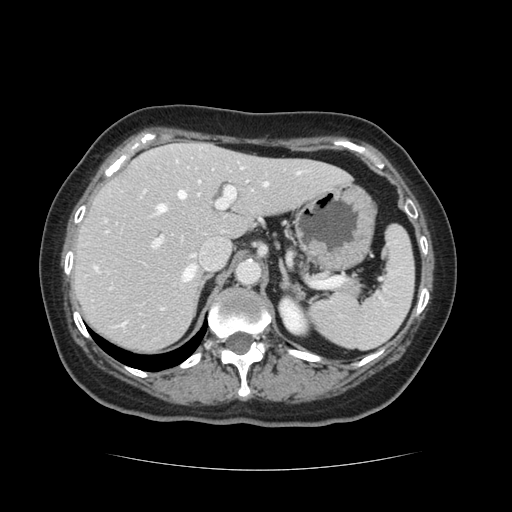
Contrast-enhanced abdominal CT, one axial slice; position 85 of 128 along the scan axis; 120 kVp; intravenous contrast given; soft-tissue window (W 400 / L 40 HU); 2.5 mm slice thickness; 512 × 512 image matrix. Female patient, age 67 years. From the clinical record (not read from this slice): diagnosis: colorectal cancer liver metastases, imaged before liver resection; multiple liver metastases: yes; largest metastasis: 3 cm; disease in both lobes: yes.
Structures marked on this image (manually delineated by an expert):
- hepatic veins: box from (x=157, y=173) to (x=300, y=282) px
- liver: (x=74, y=145)–(x=346, y=352)
- planned liver remnant (the part of the liver to remain after resection): (x=74, y=157)–(x=346, y=352)
- portal vein (with intrahepatic branches): (x=155, y=168)–(x=248, y=246)